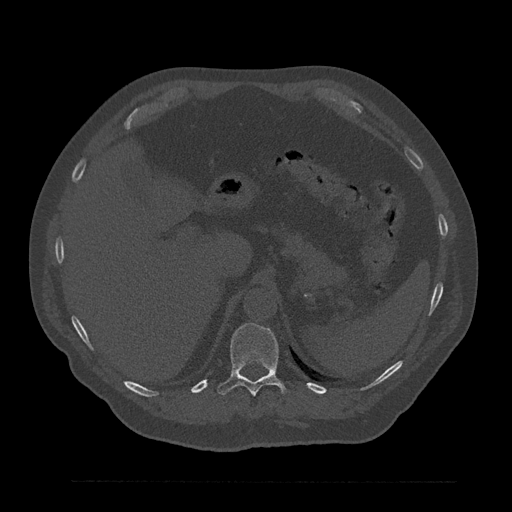
CT including the spine, one axial slice. Position 293 of 797 along the scan axis. Reconstruction kernel Br40s/3. Bone window (W 1800 / L 400 HU). 0.5 mm slice thickness. 512 × 512 image matrix. Male patient, age 61 years. From the clinical record (not read from this slice): primary cancer: prostate.
Annotated regions visible in this slice (semi-automatic segmentation, software-assisted and operator-edited):
- T11 vertebra: box from (x=217, y=322) to (x=288, y=396) px